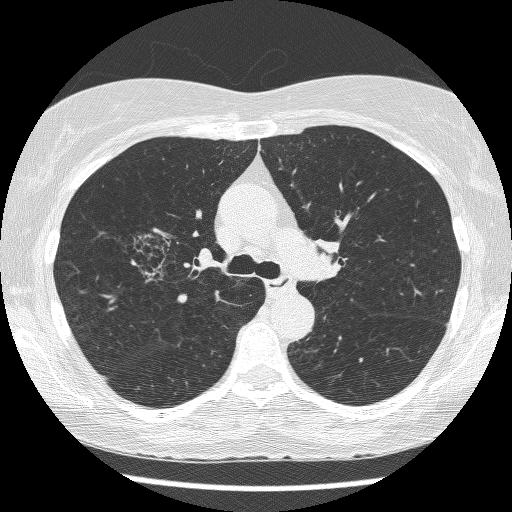
Axial slice from a low-dose chest CT screening exam, baseline annual screen, lung window (W 1500 / L -600 HU), lung (sharp) reconstruction kernel (BONE), slice 182 of 271 in the series, 512 × 512 image matrix. Female, age 64 years at enrolment.
Lesion marked by an expert reader, bounding box [x1, y1, x2, y2] px = [126, 225, 207, 300]. The screening reader recorded 3 non-calcified nodules or masses ≥4 mm on this exam (right upper lobe, right upper lobe, left lower lobe); which of them this box marks is not recorded. Later outcome: lung cancer diagnosed 735 days after this screen — adenocarcinoma, NOS, right upper lobe, right middle lobe, right hilum, stage IV (AJCC 6th edition), 85 mm at pathology.